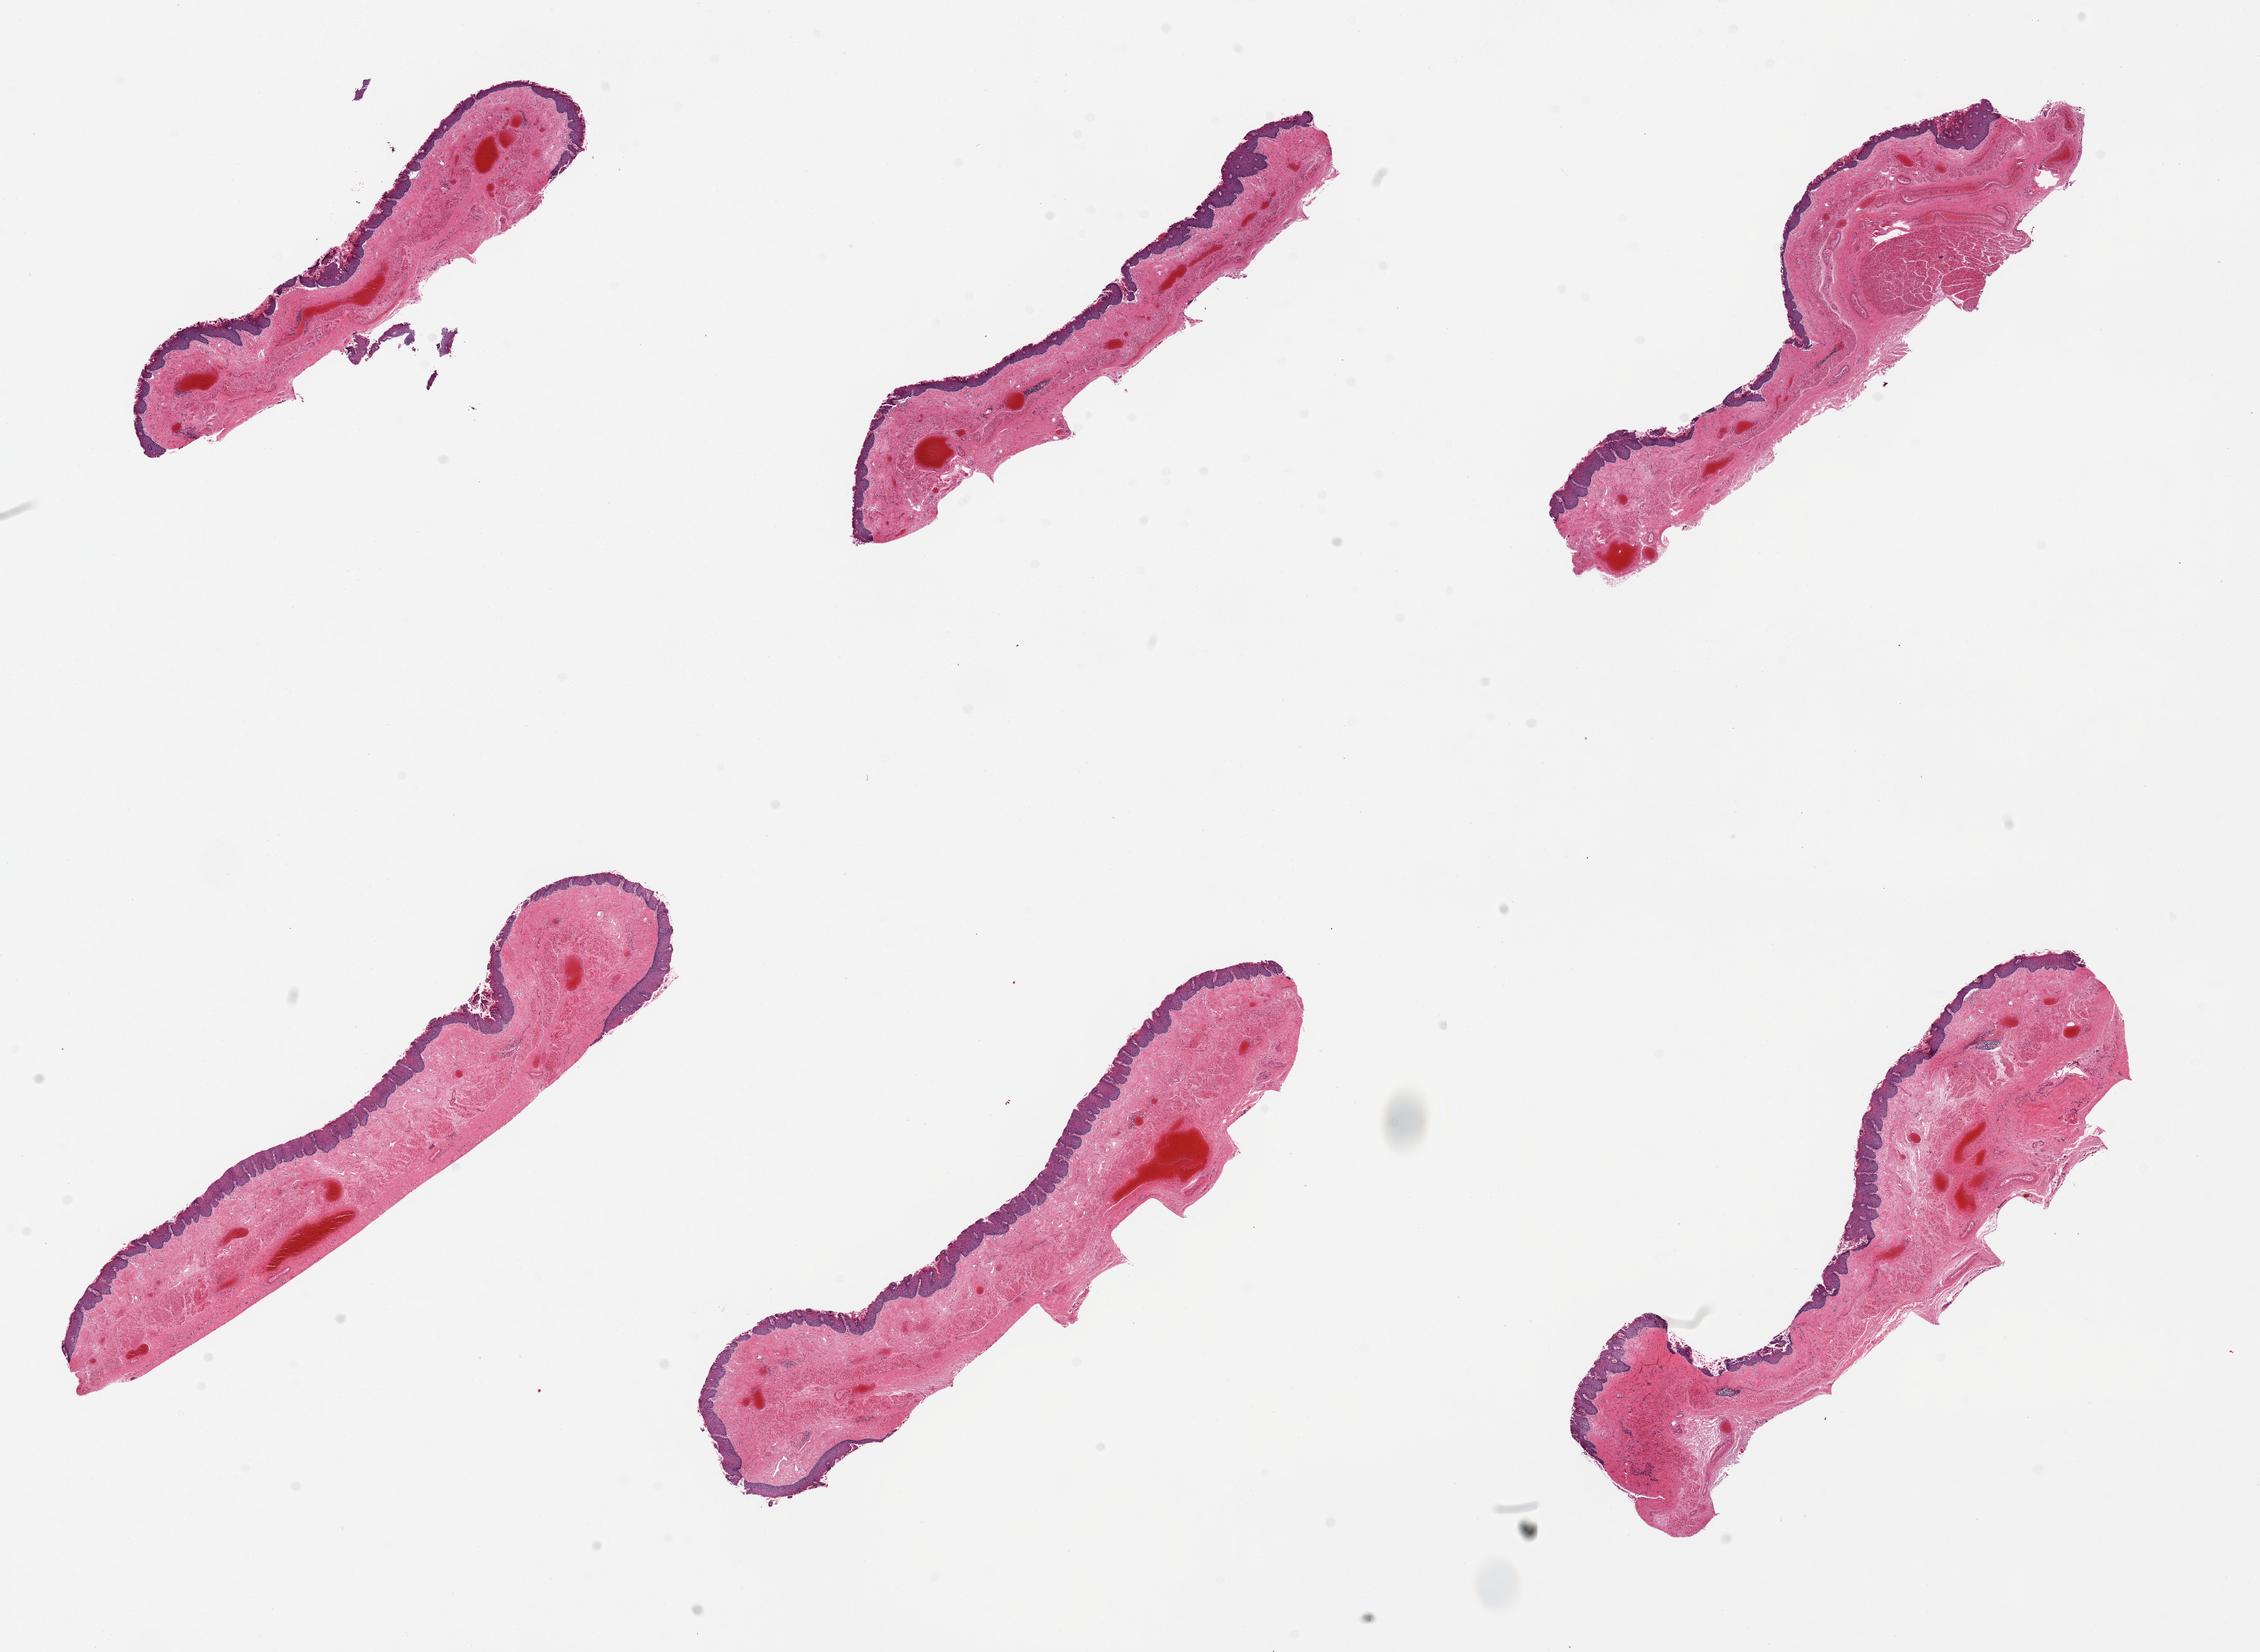
Hematoxylin and eosin (H&E) whole-slide image — shown as a low-resolution overview of the whole scanned area (about 24.6 x 18.0 mm); PAXgene-fixed paraffin-embedded (PFPE) section; sampled site (target tissue): esophageal mucous membrane; tissue donor sample. Male donor.
- pathologist's review note for this sample: 6 pieces, squamous mucosa is ~0.2mm, in some foci approaching autolysis score 2, early separation/sloughing noted